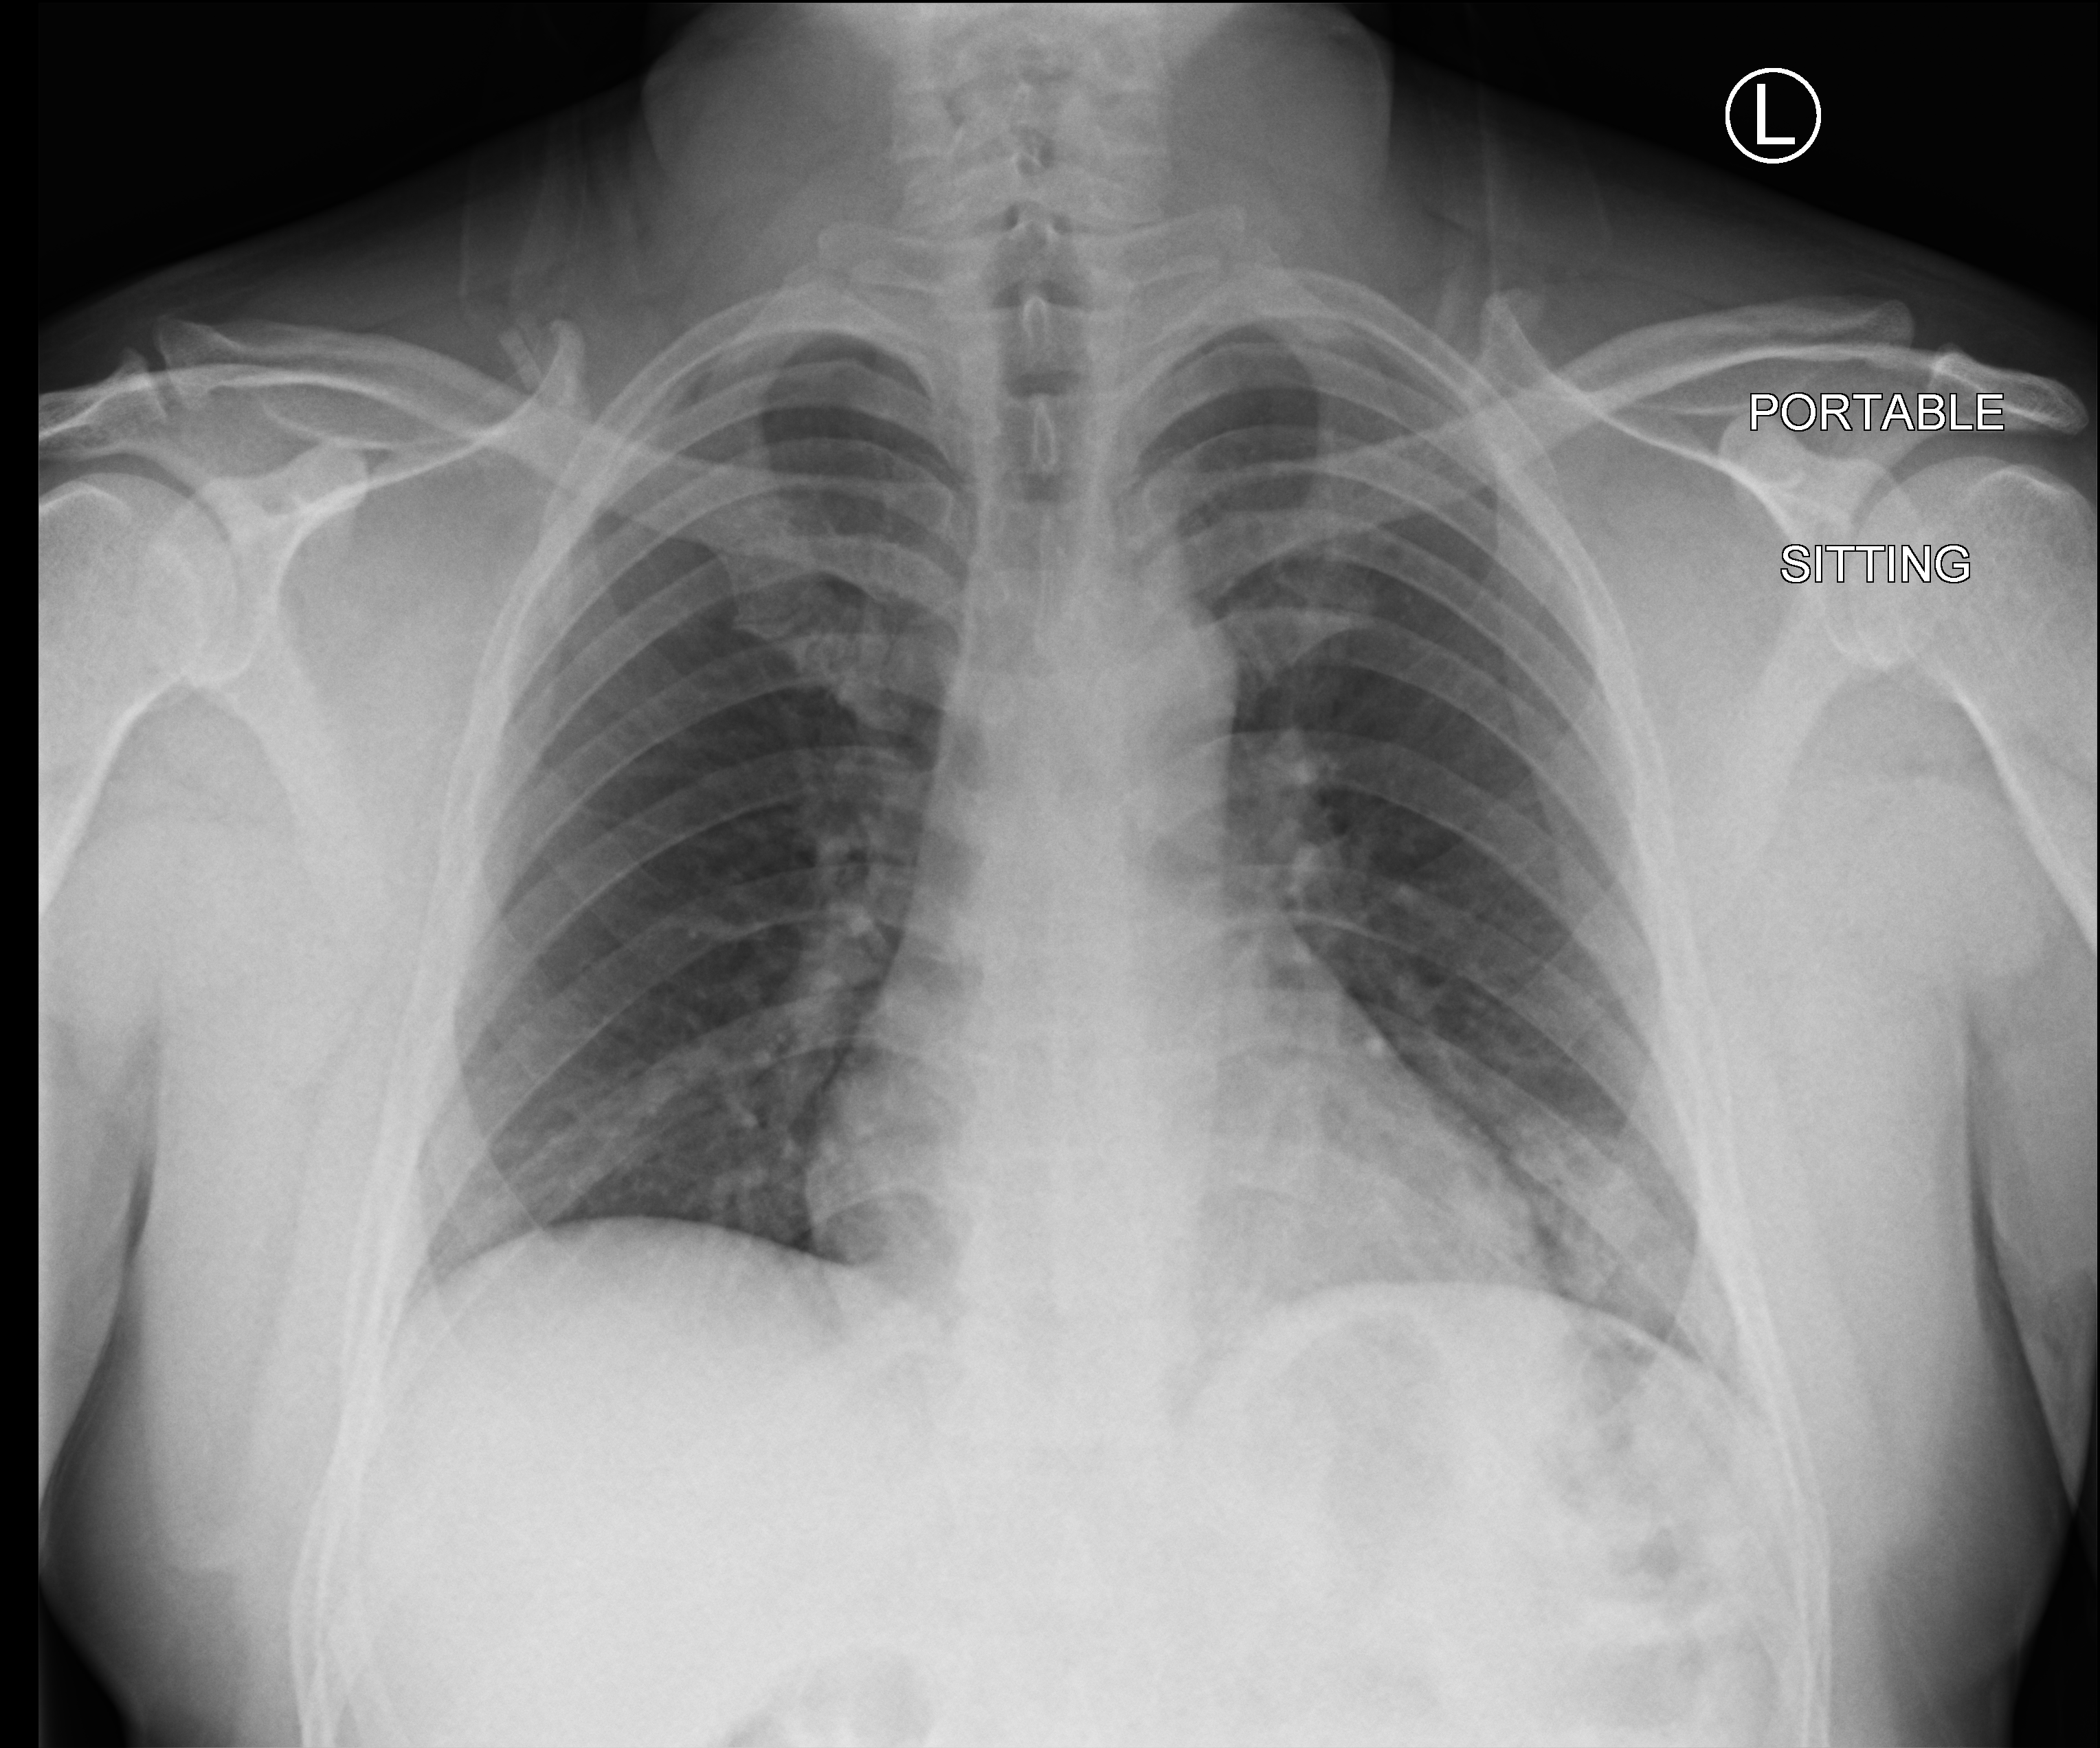
Bedside chest radiograph (computed radiography), anteroposterior (AP) projection. Male patient hospitalised with COVID-19, age 18–59 years.
Hospital-stay facts (about this admission, not read from this image; timing relative to this image not recorded): admitted to intensive care during this hospital stay: no.